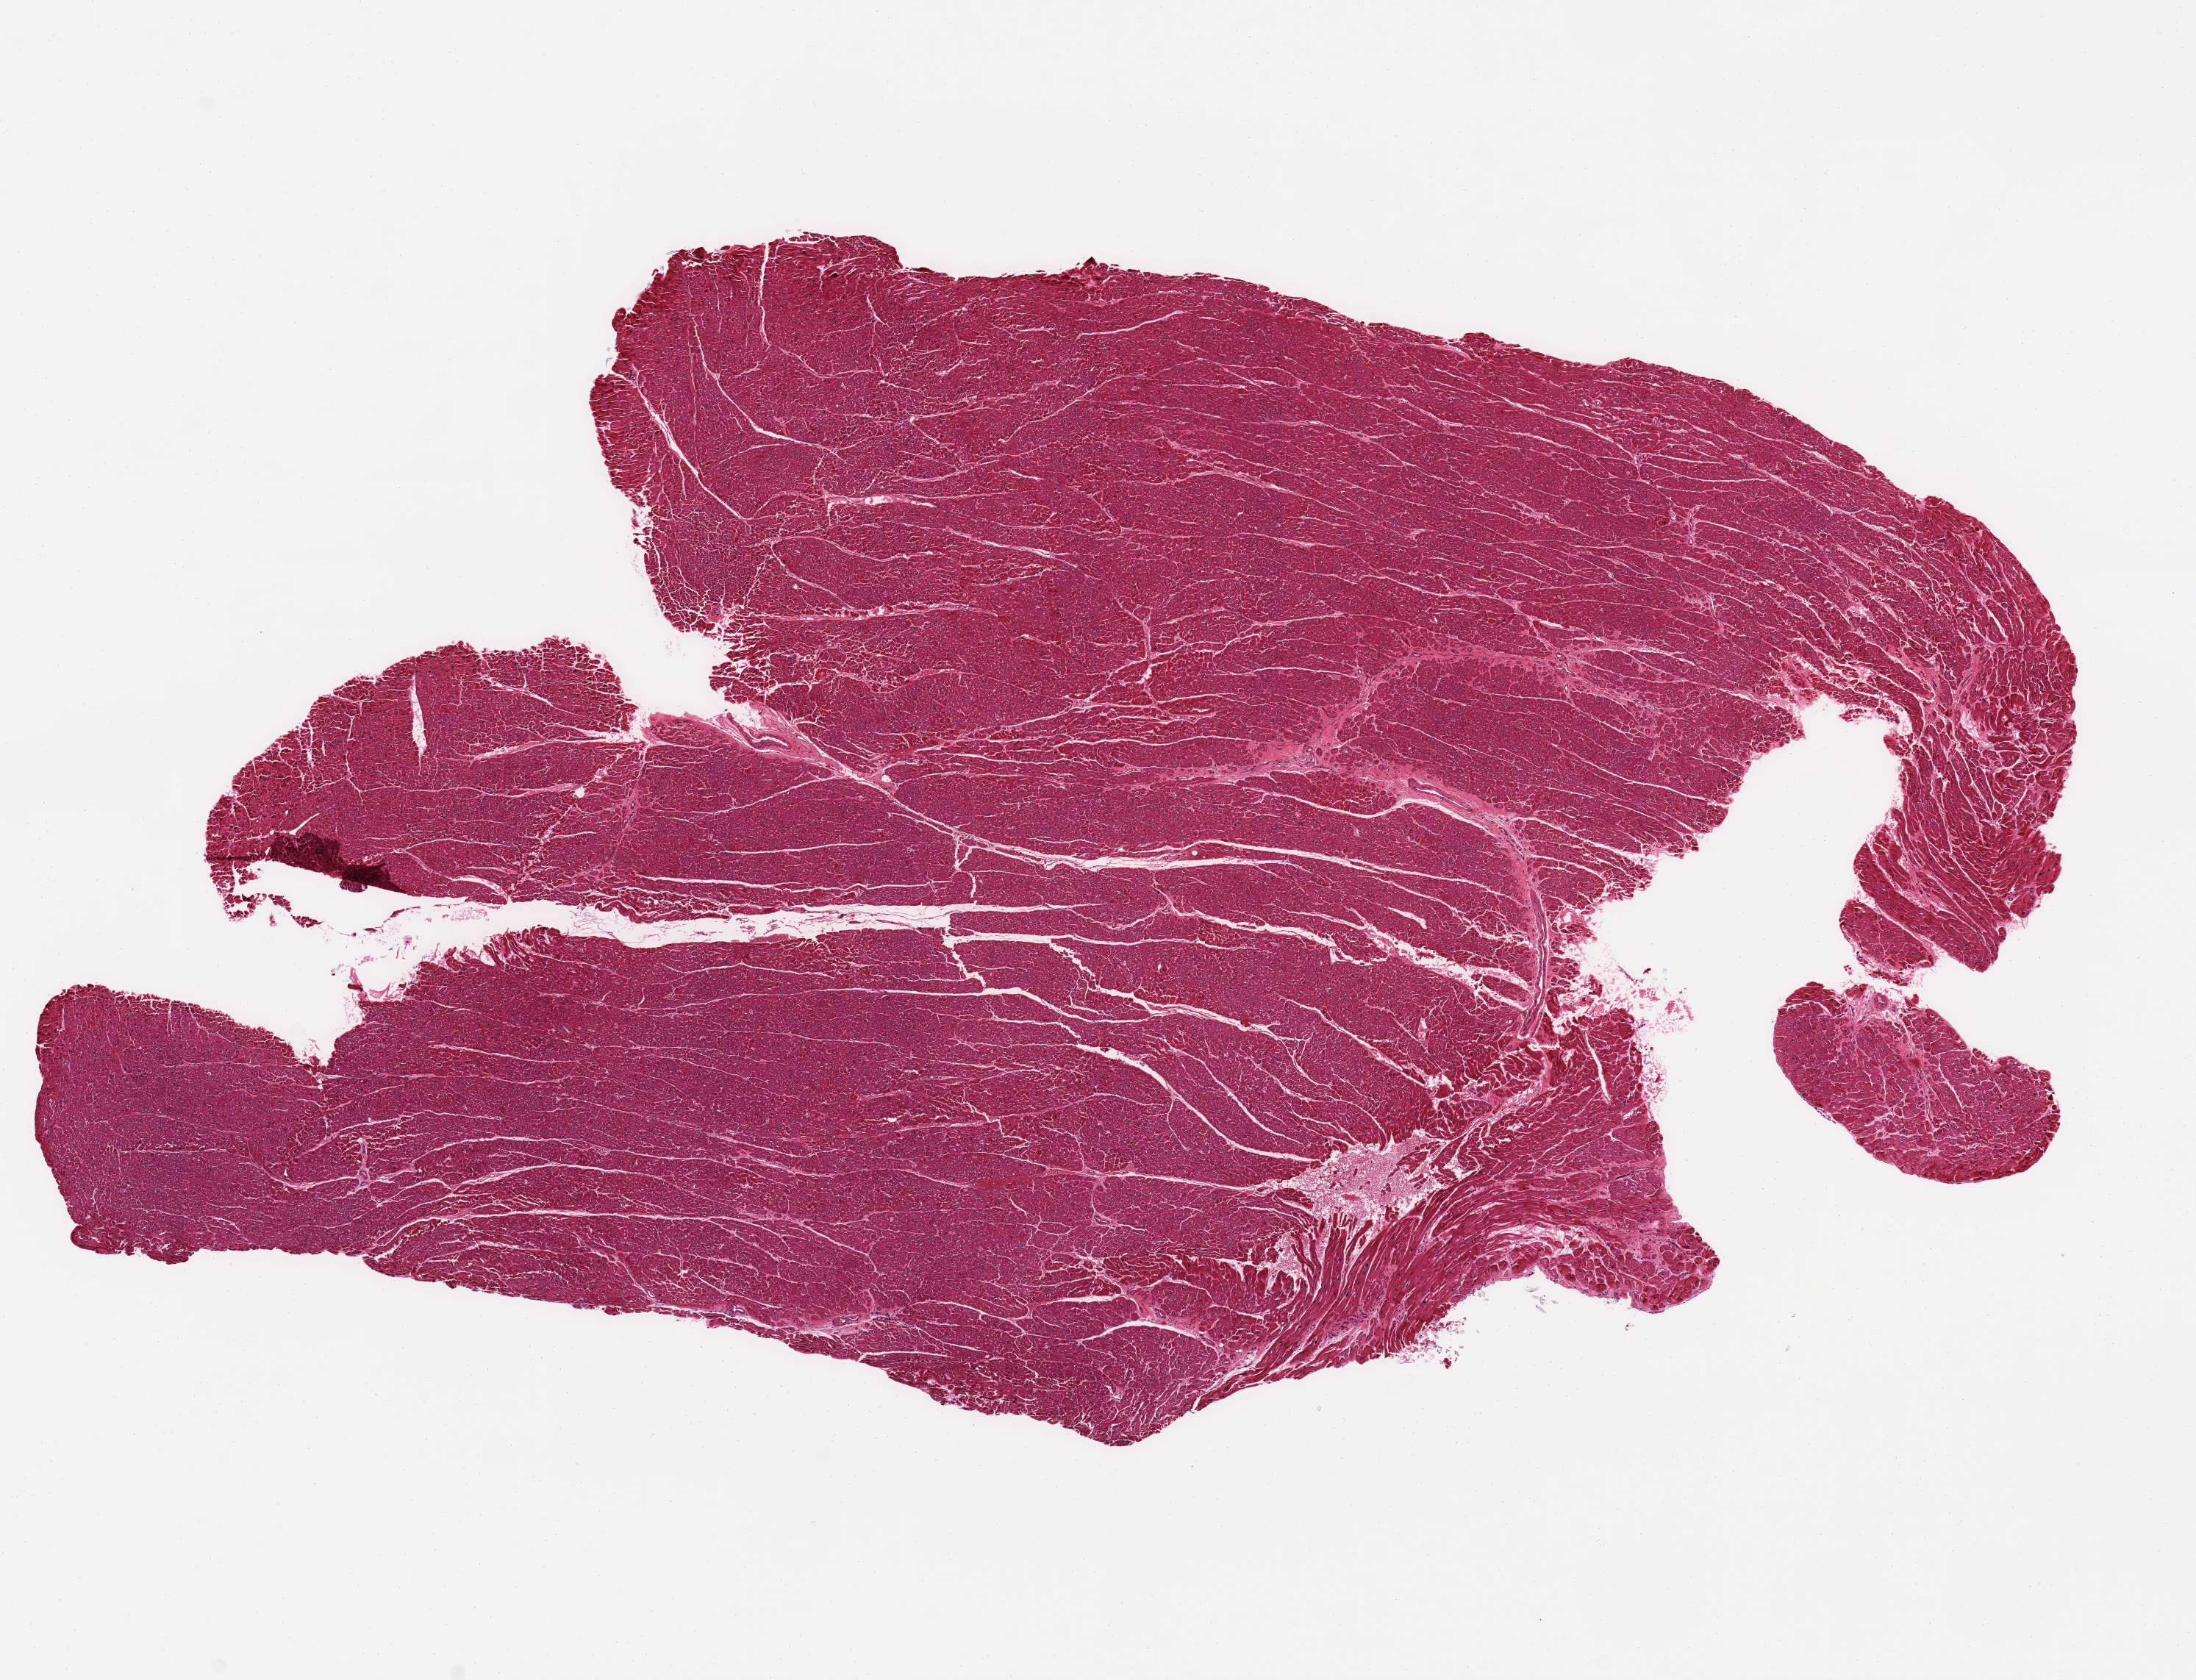
Digitized hematoxylin and eosin (H&E)-stained section — shown as a low-resolution overview of the whole scanned area (about 11.8 x 9.0 mm), PAXgene-fixed, paraffin-embedded tissue, sampled site (target tissue): heart, tissue donor sample. Donor sex: female.
• reviewer comment on this tissue sample: Hypertrophic nuclei